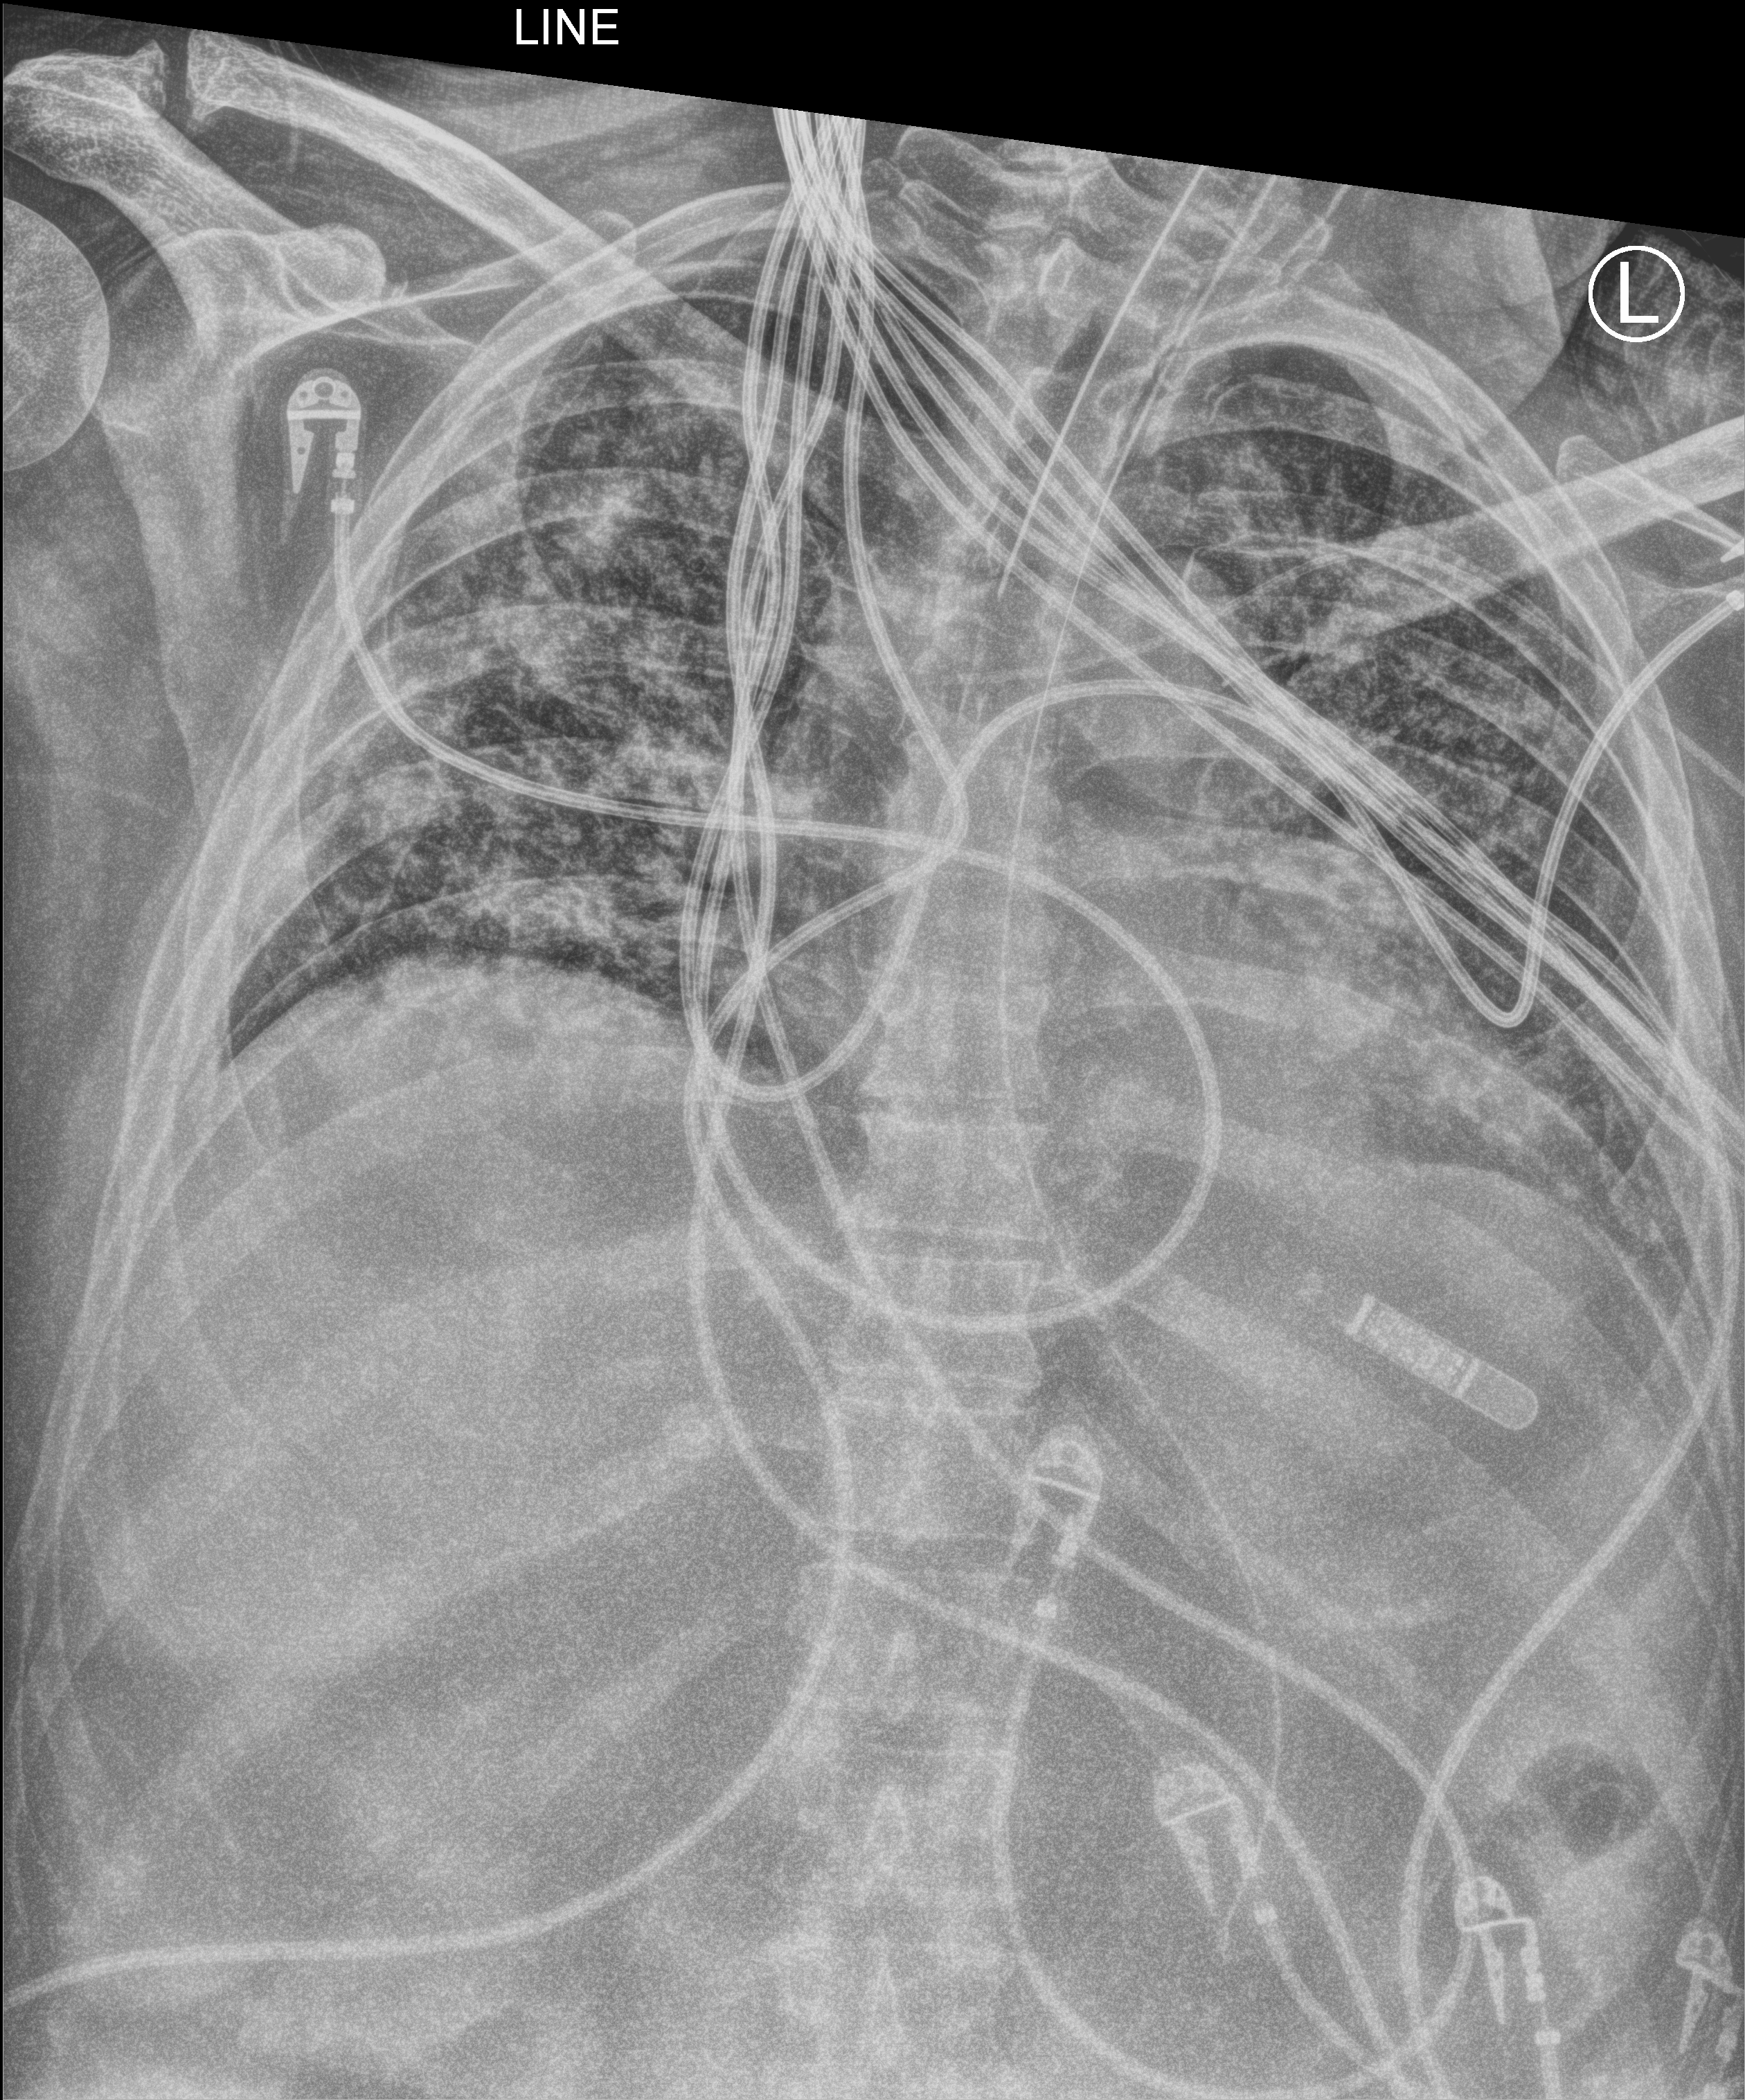
Bedside chest radiograph (computed radiography), anteroposterior (AP) projection. Male patient hospitalised with COVID-19, age 18–59 years.
Admission-level facts for this patient (not findings on this image; timing relative to this image not recorded):
- admitted to intensive care during this hospital stay: yes
- mechanically ventilated during this hospital stay: yes
- diabetes (admission record): no